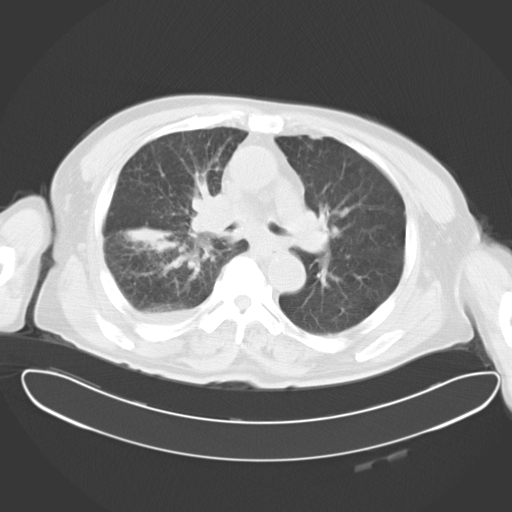
Chest CT, one axial slice; slice 18 of 30 in the series (ordered by position); reconstruction kernel B40f; 120 kVp; lung window (W 1500 / L -600 HU); 512 × 512 image matrix. Patient: male, 78 years. From the clinical record (not read from this slice): clinical TNM (as recorded): T2 N1 M1.
Outlined on this slice (rectangle marked by the reading radiologist):
- lung tumour (recorded histology: adenocarcinoma): box from (x=123, y=192) to (x=237, y=279) px